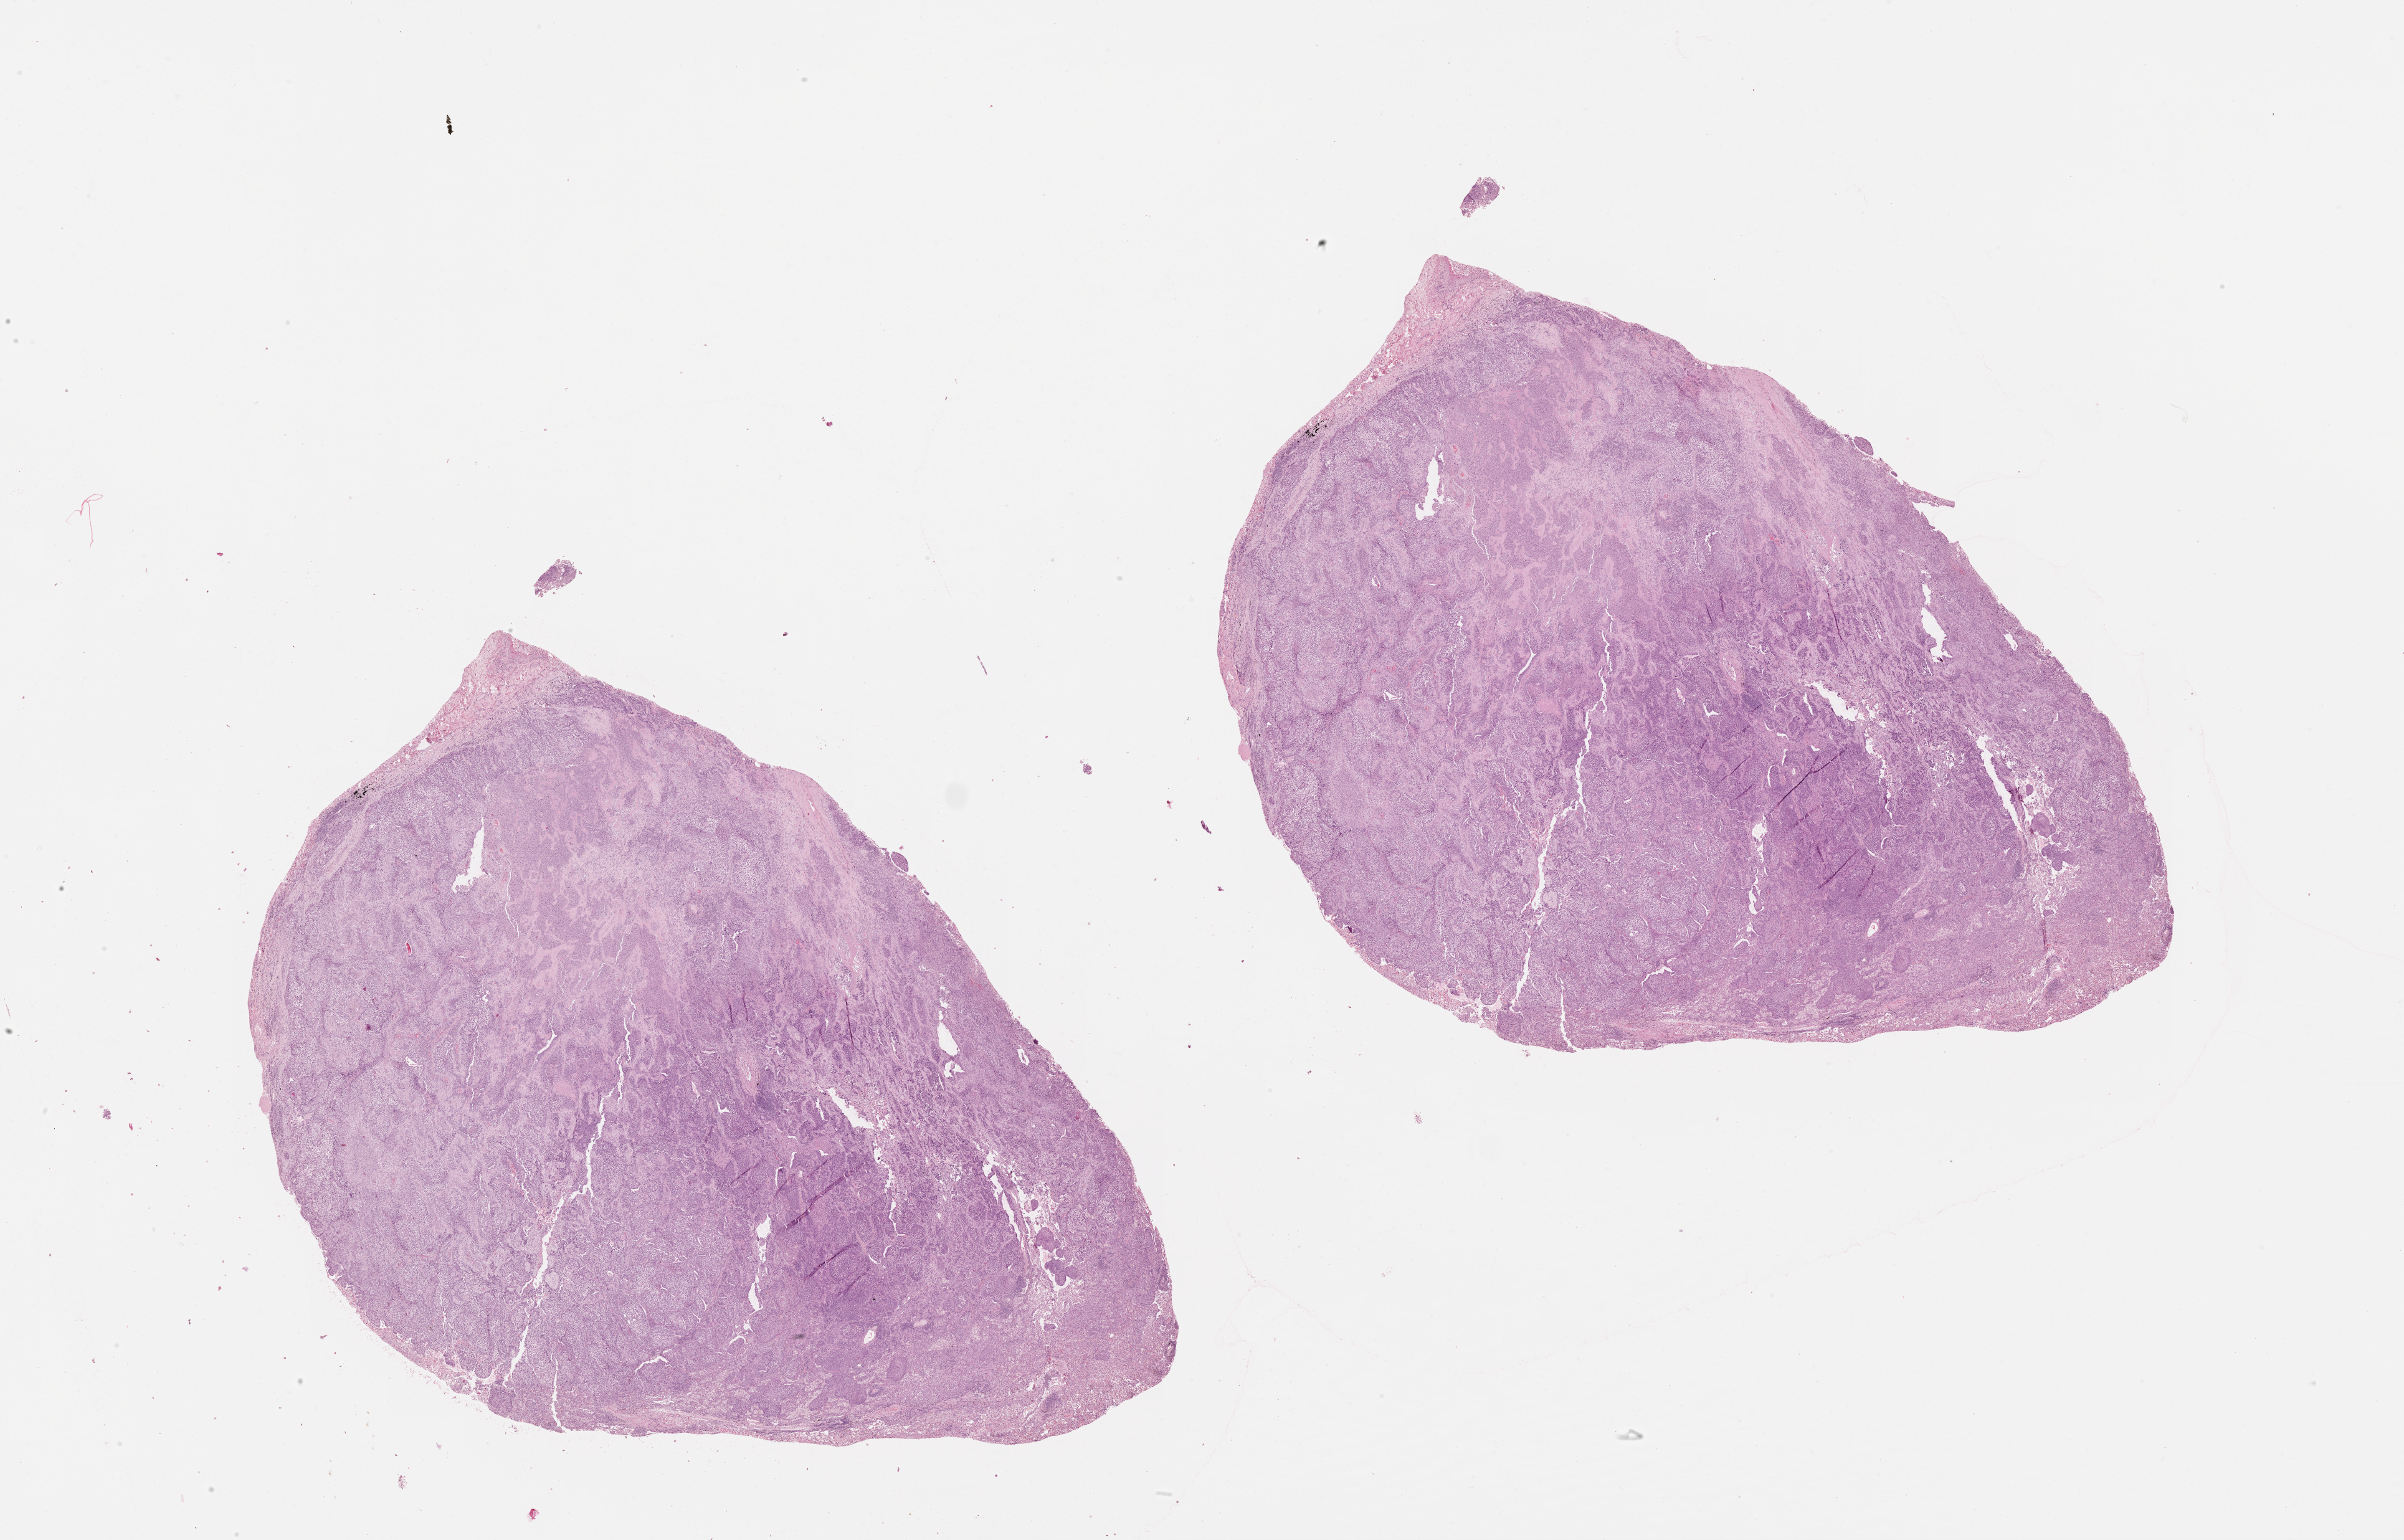
Whole-slide histology image, H&E — whole scanned area (about 31.1 x 19.9 mm) shown as a low-resolution overview. Tumour tissue sample, lung. Patient: male, age 56 years.
Patient diagnosis (cohort enrolment): squamous cell carcinoma (lung).